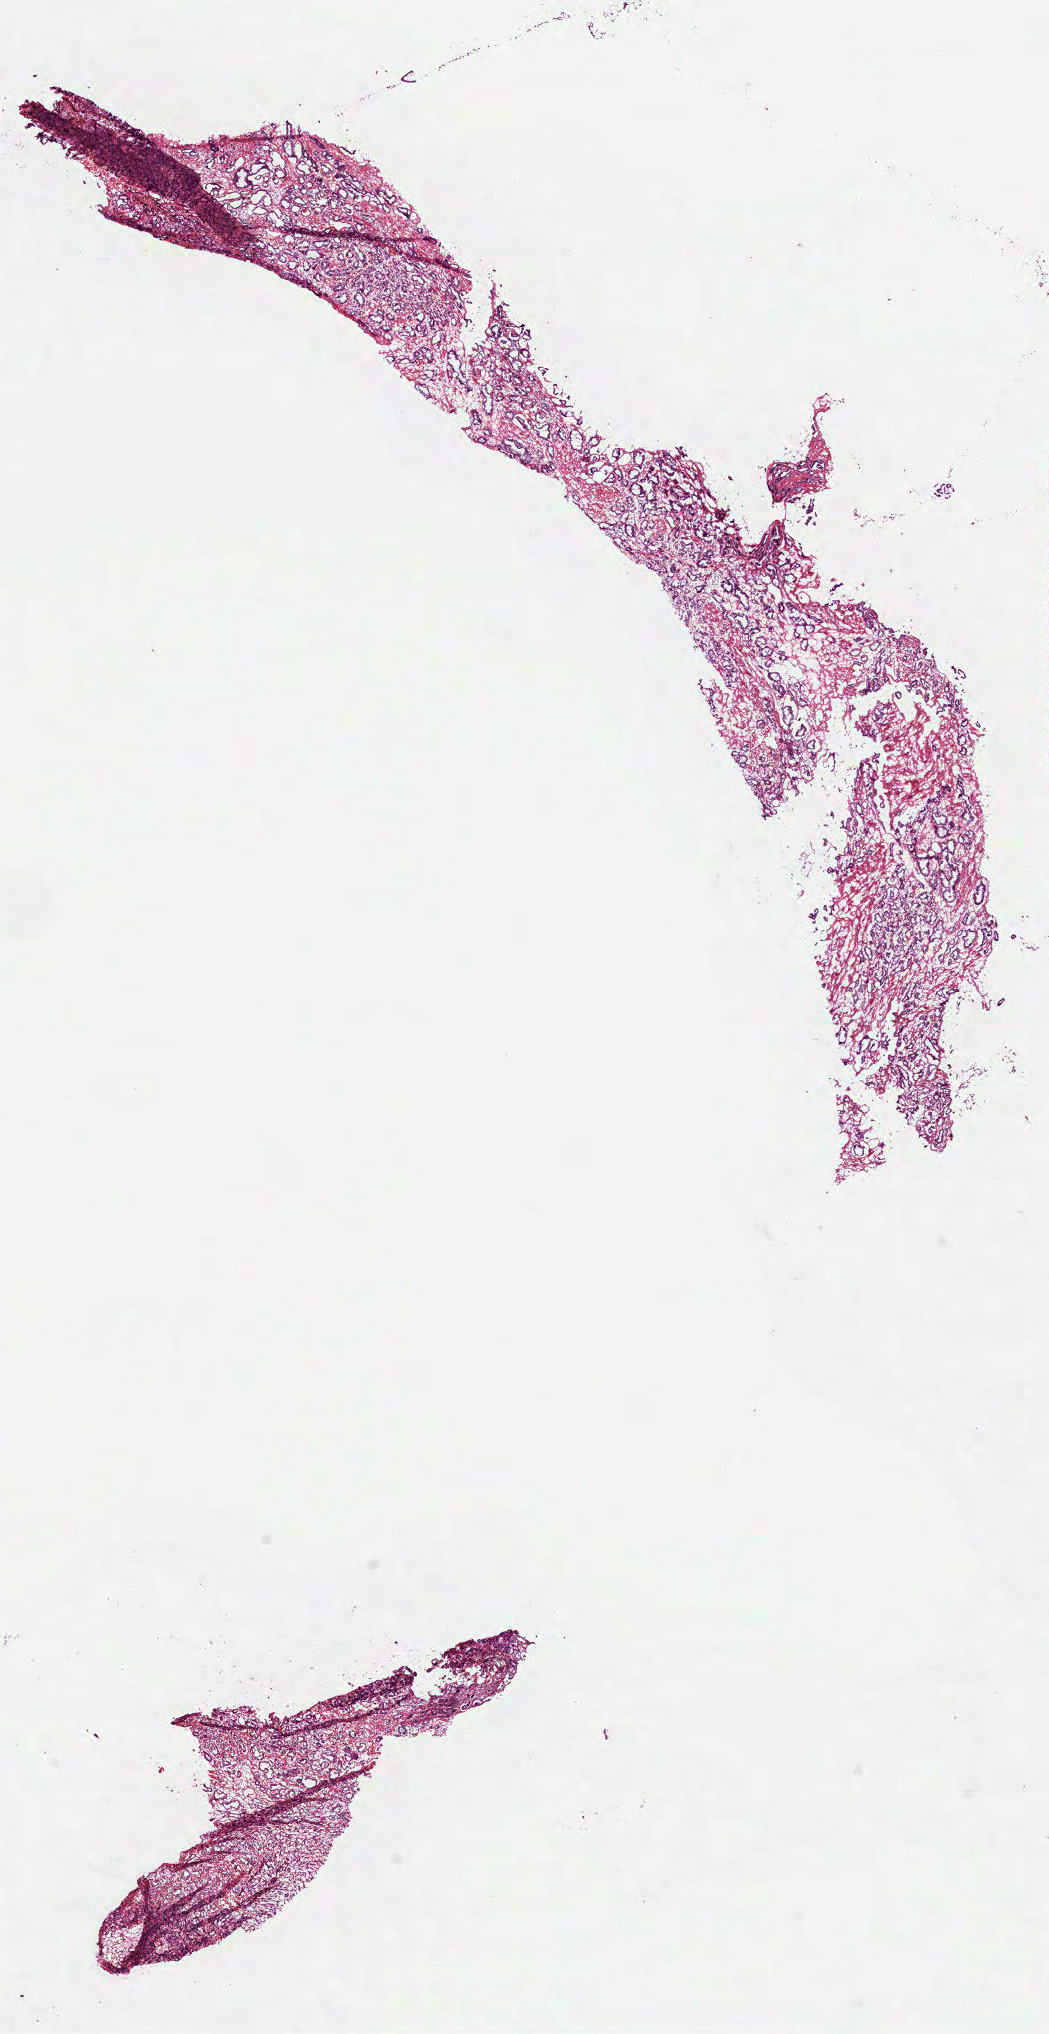
Whole-slide histology image, H&E, a low-resolution overview of the entire scanned area, about 8.5 x 16.4 mm. Frozen section from the bottom of the tissue portion. Prostate, primary tumour sample. Male patient; age at initial diagnosis 44 years. Gleason score: 7 (3+4). Slide review estimates, as recorded: tumour cells 70%, tumour nuclei 70%, normal cells 5%, stromal cells 25%, necrosis 0%.
Lymph nodes positive (case pathology): 0 of 13 examined. Laterality: bilateral. Histologic diagnosis: Acinar cell carcinoma (prostate gland).